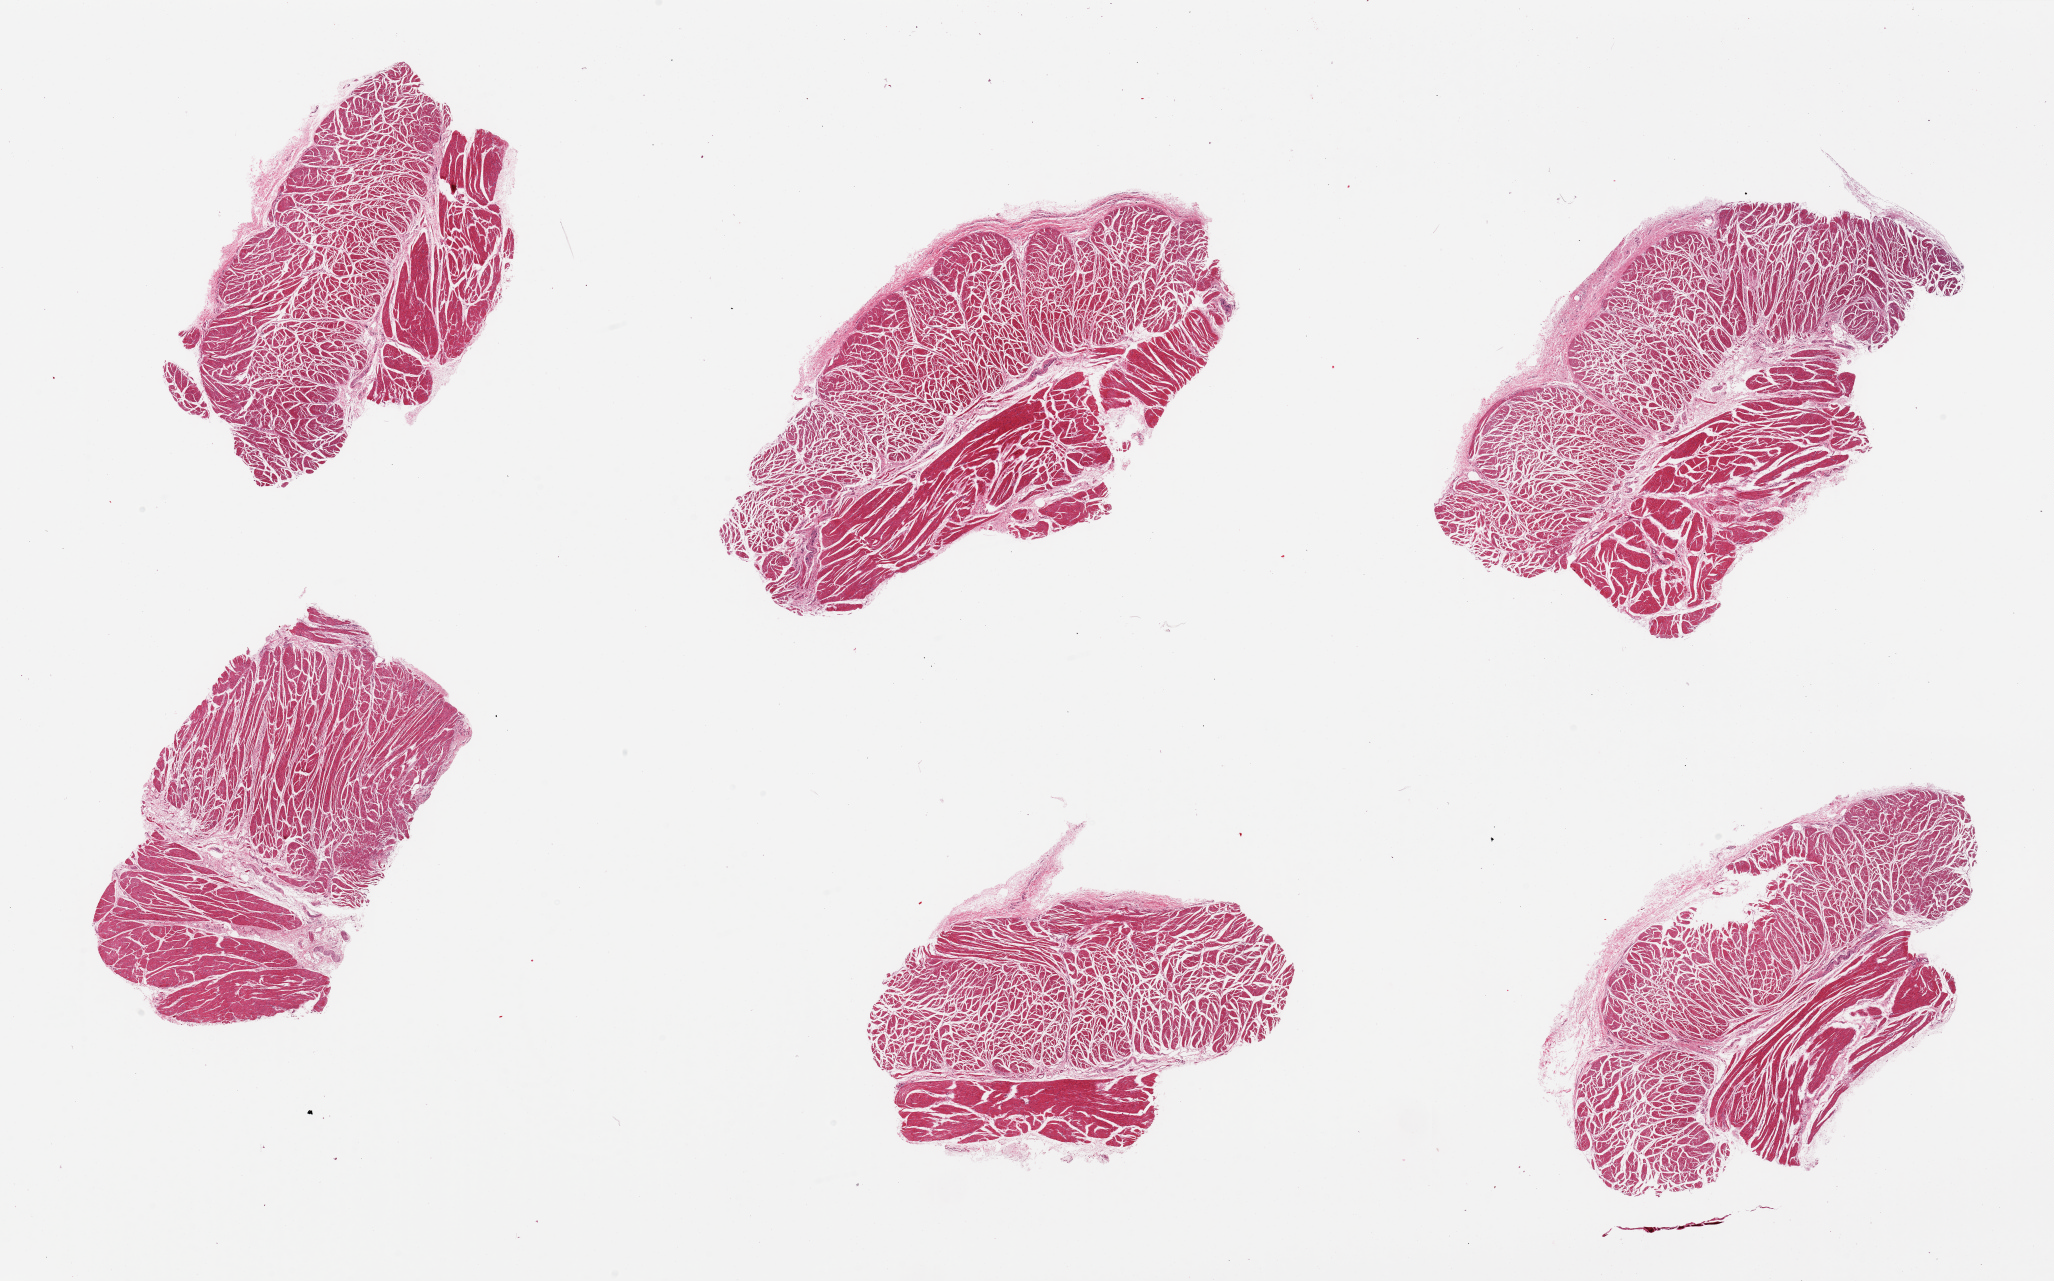
Digitized haematoxylin and eosin-stained section, low-resolution overview of the scanned area, about 32.5 x 20.3 mm; PAXgene-fixed paraffin-embedded (PFPE) section; target tissue: esophageal muscle; donor tissue sample.
Reviewer comment on this tissue sample: 6 pieces, good specimens, no mucosa seen.